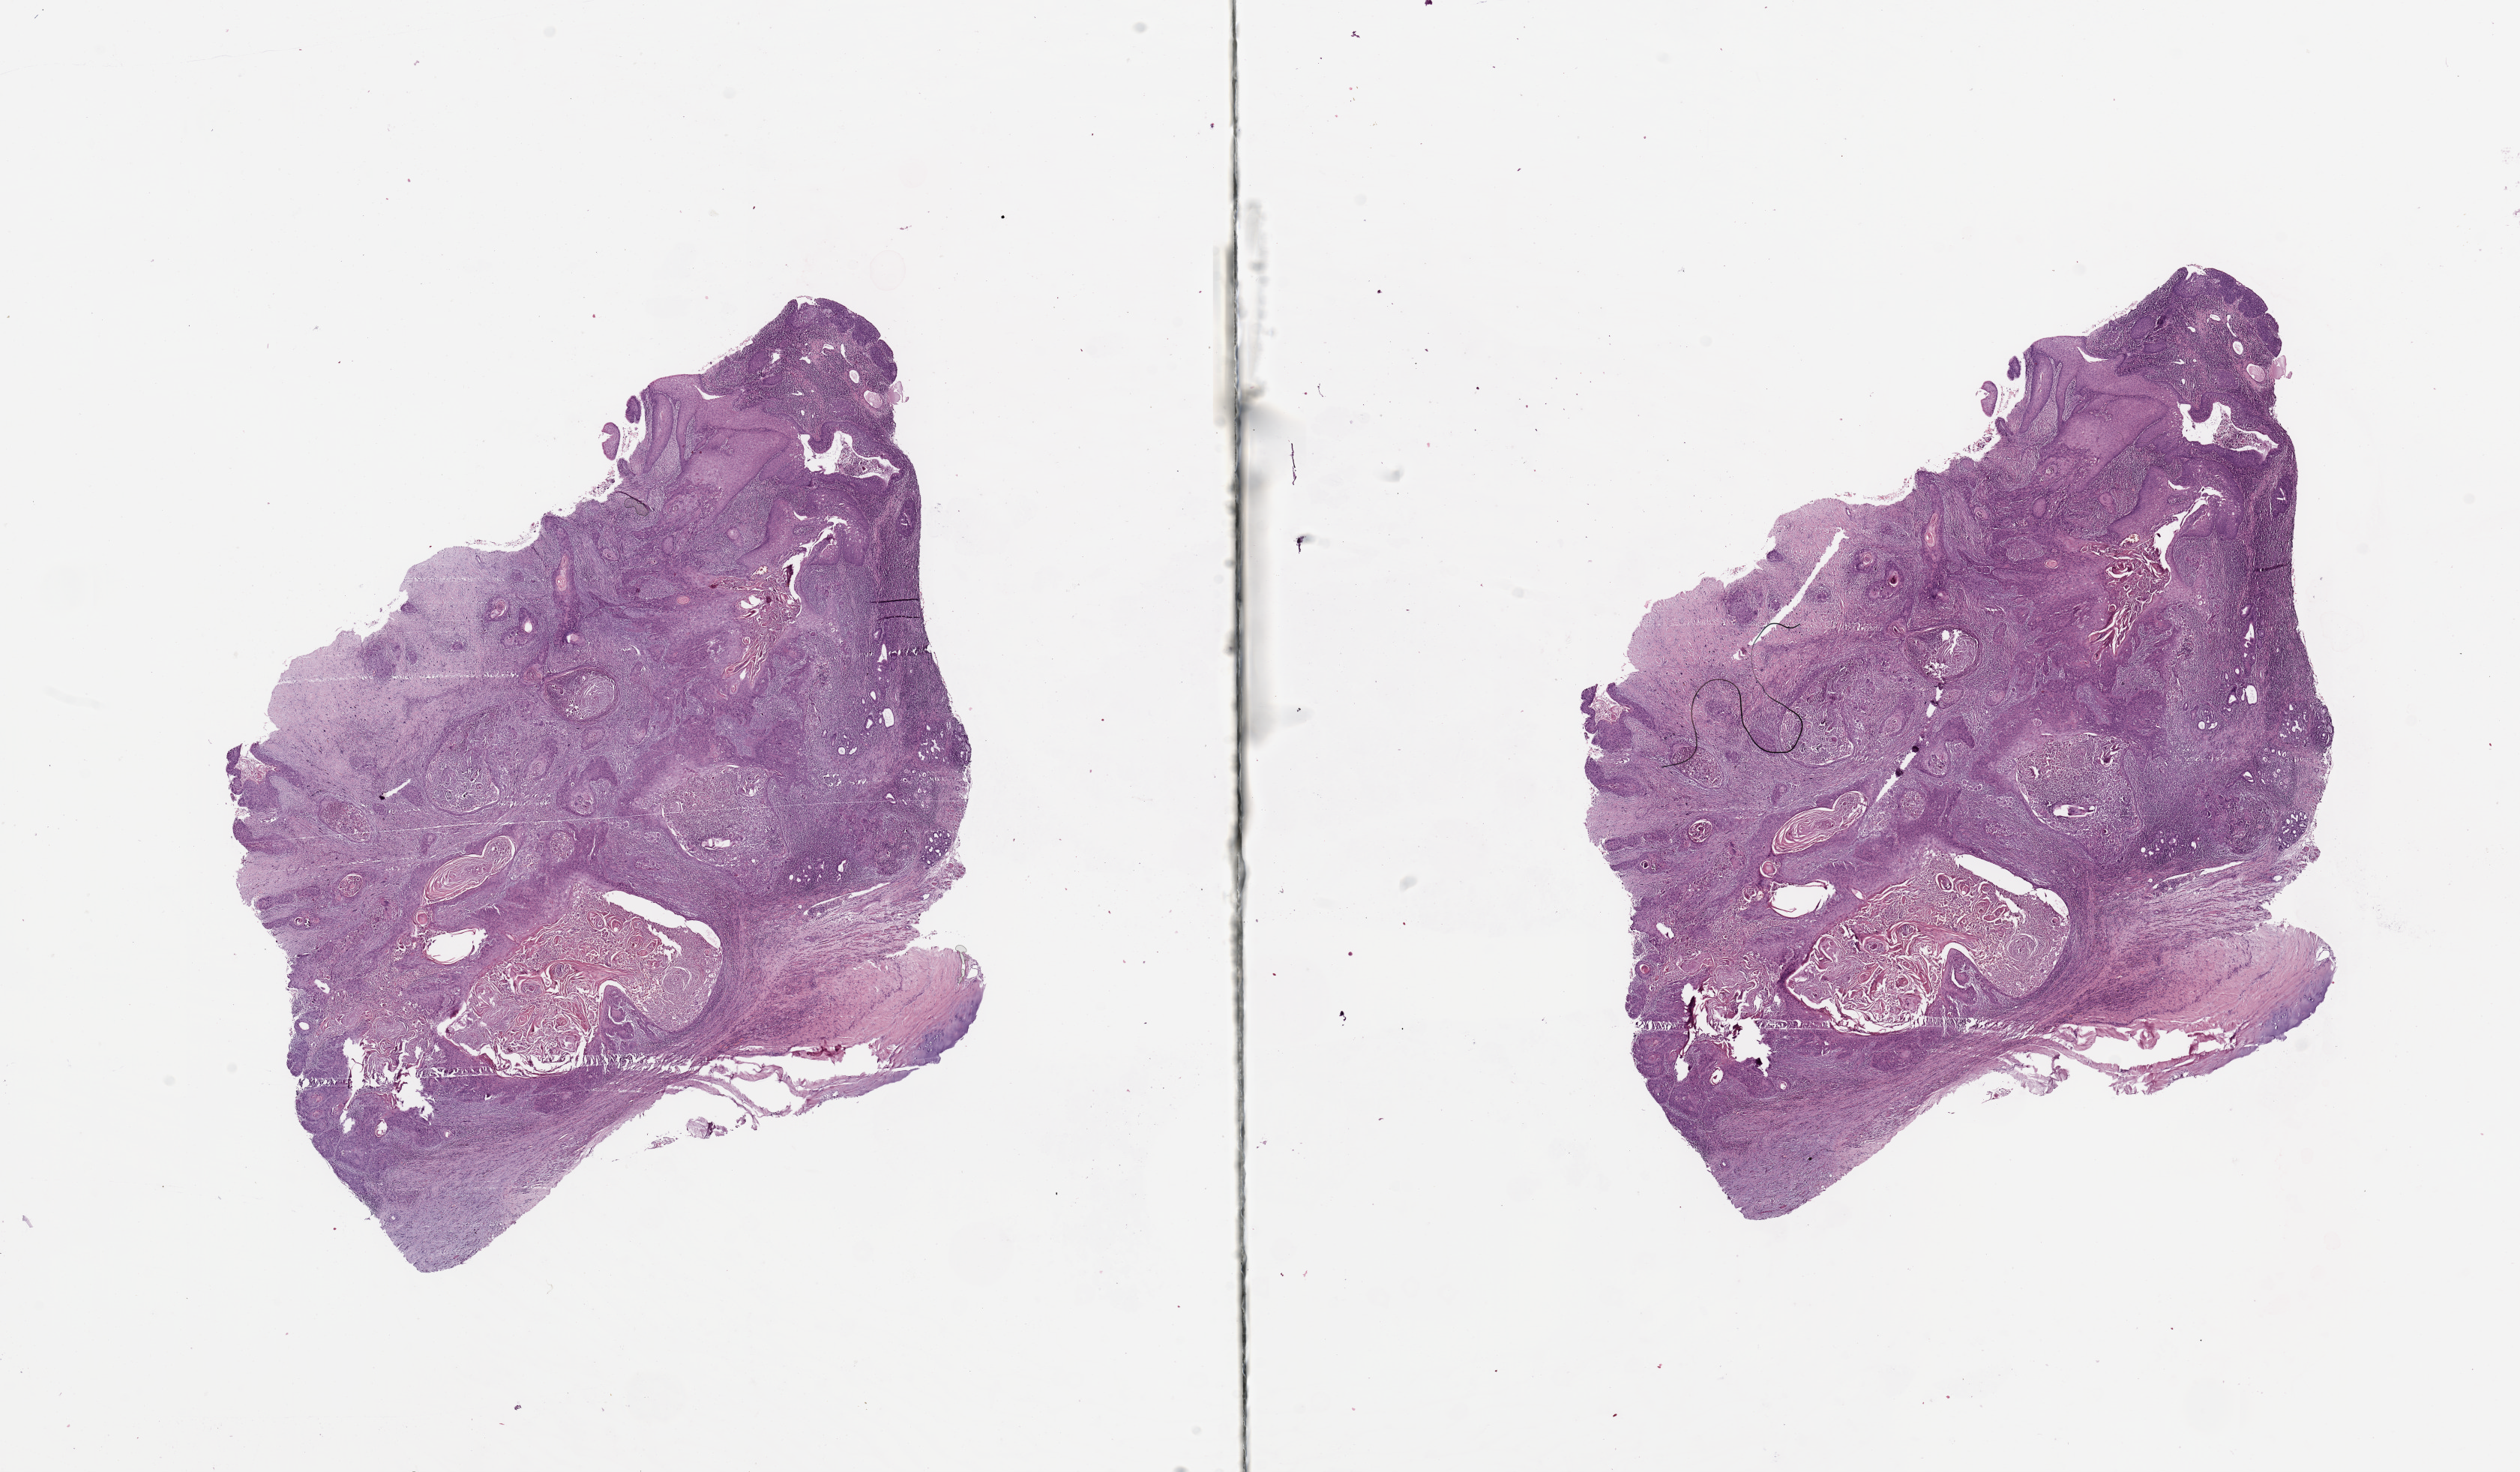
Digitized Hematoxylin and eosin (H&E) stained tissue section (whole slide) — a low-resolution overview of the entire scanned area, about 26.6 x 15.5 mm (acquisition: 20x scan). Head and neck, tissue type not recorded. 49-year-old male patient.
• patient diagnosis: Squamous cell carcinoma, NOS (larynx, NOS)